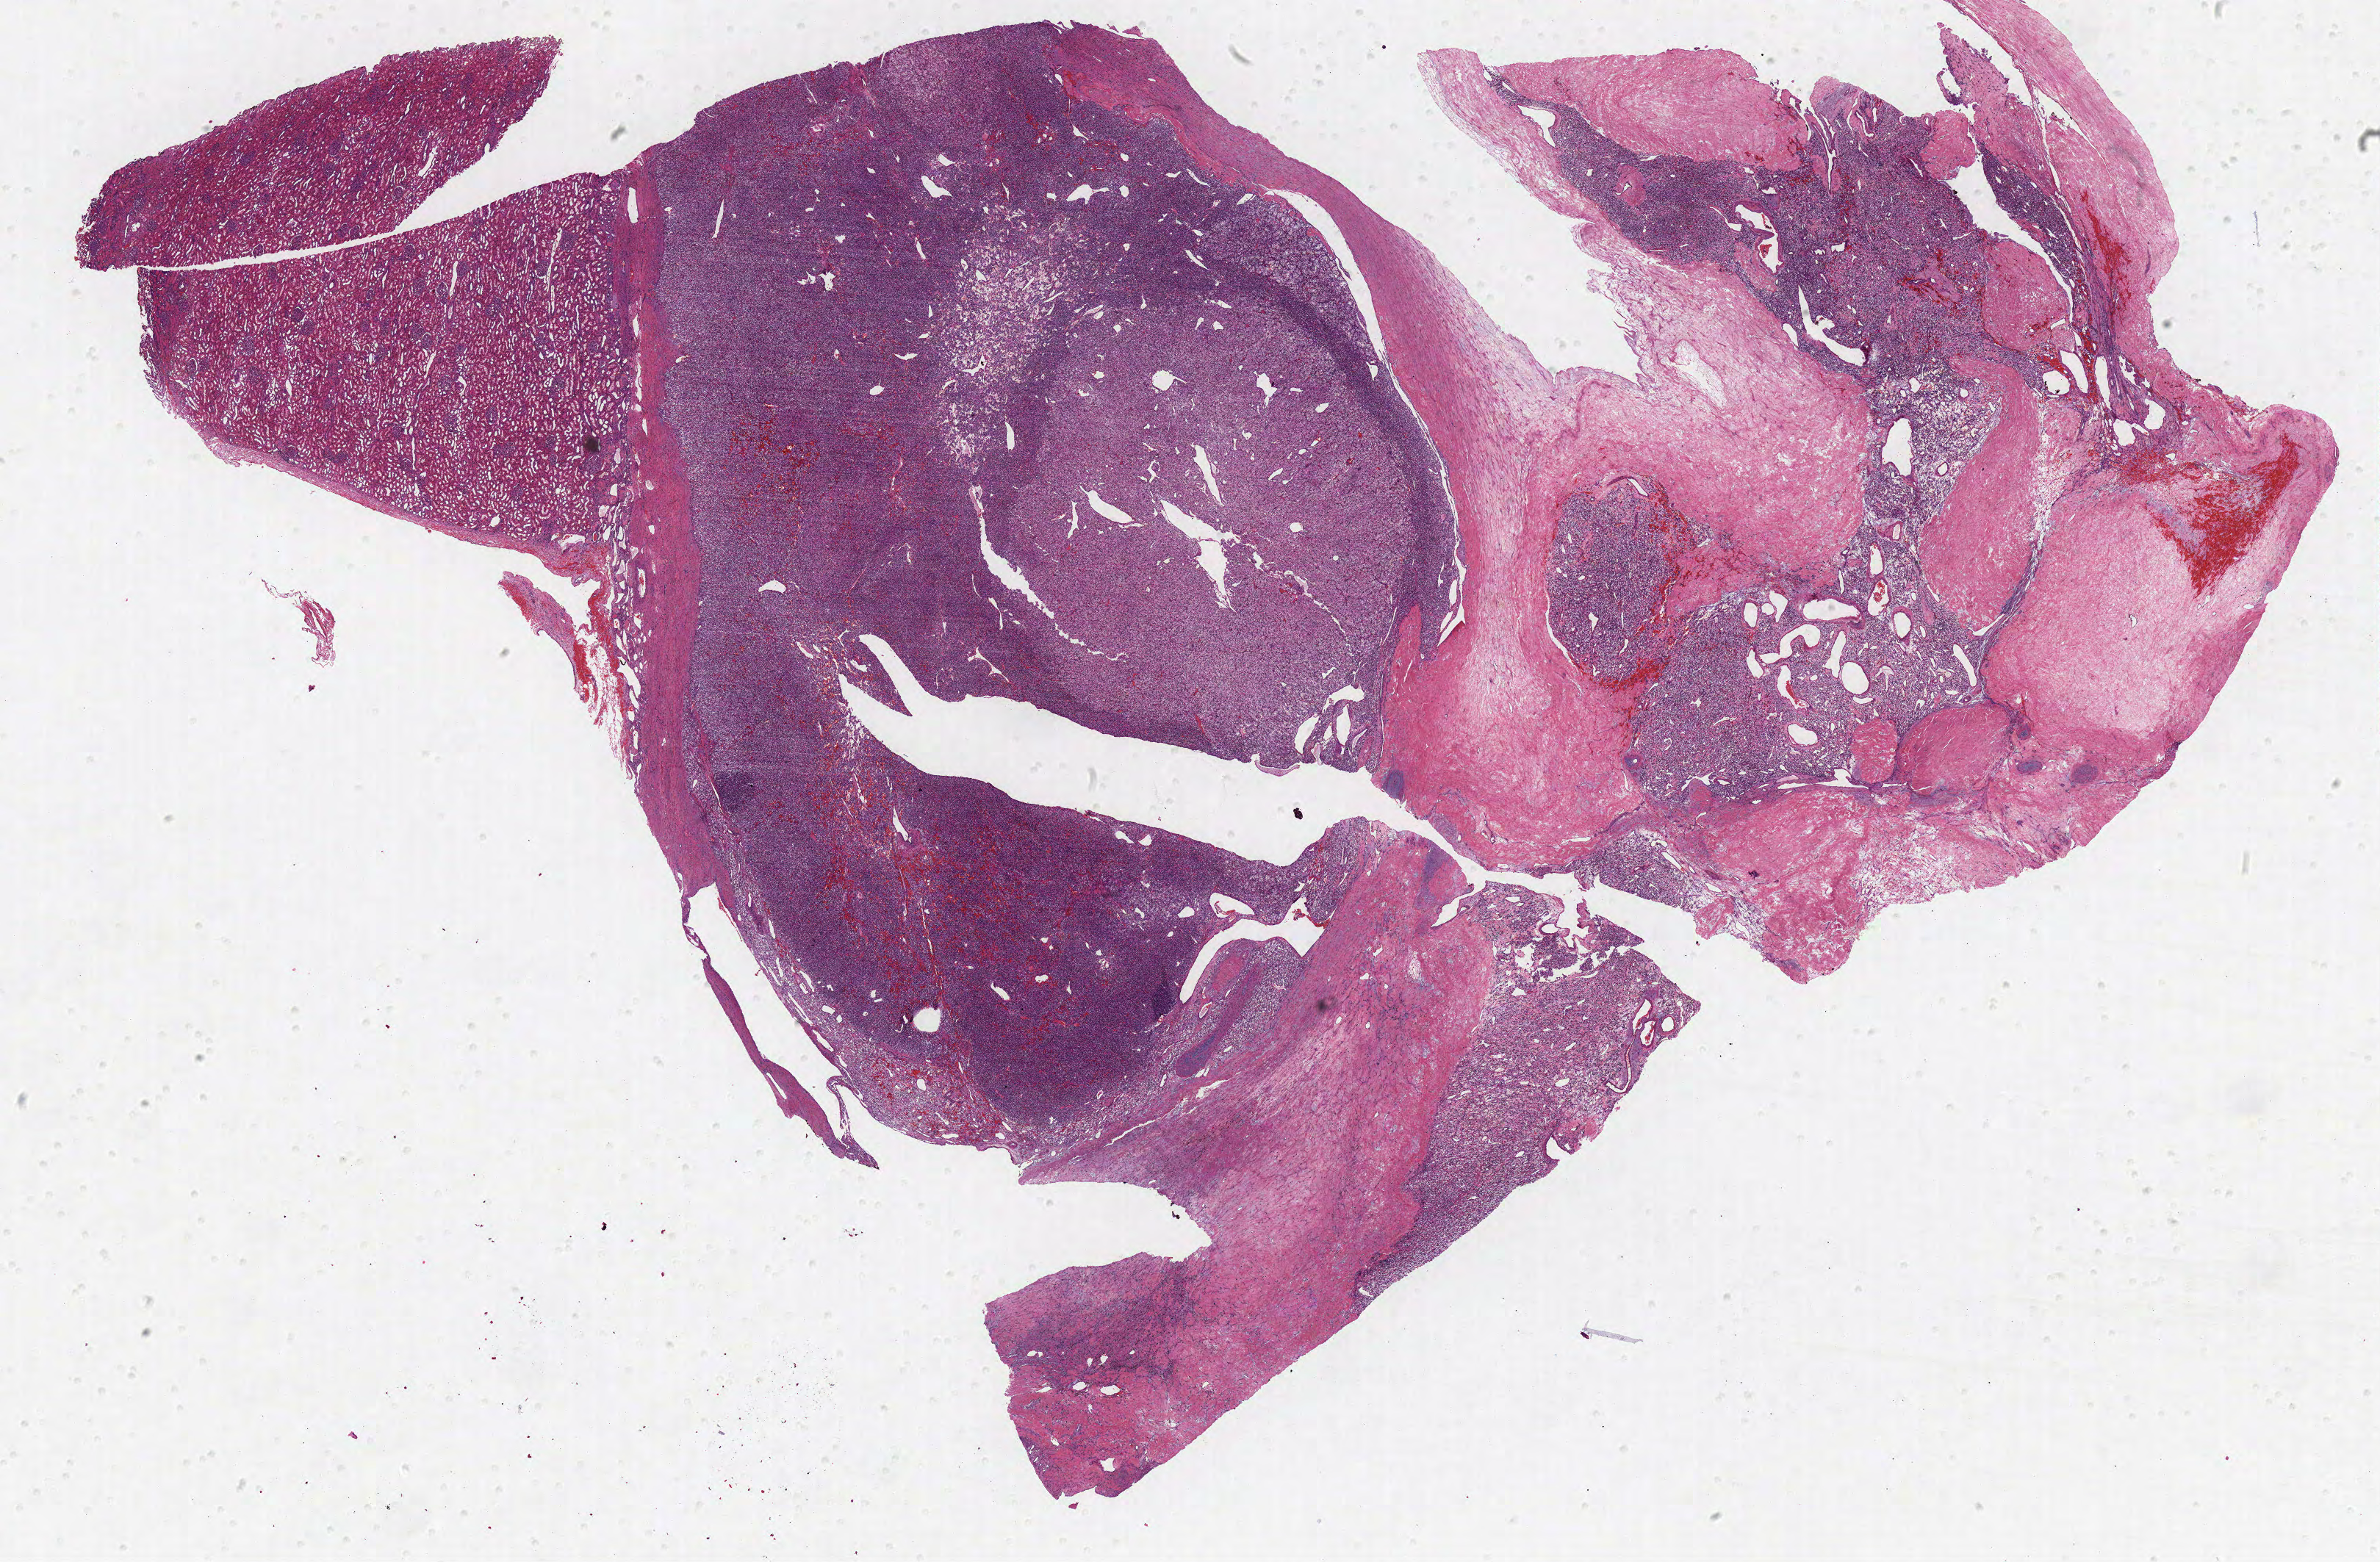
H&E-stained whole-slide image, whole scanned area (about 25.9 x 17.0 mm, acquisition: 40x scan) shown as a low-resolution overview, formalin-fixed paraffin-embedded (FFPE) diagnostic section, kidney, primary tumour sample. Male, age 59 years at initial diagnosis. Histologic grade: G2 (moderately differentiated).
- laterality: right
- AJCC pathologic stage: I
- histologic diagnosis: Clear cell adenocarcinoma, NOS